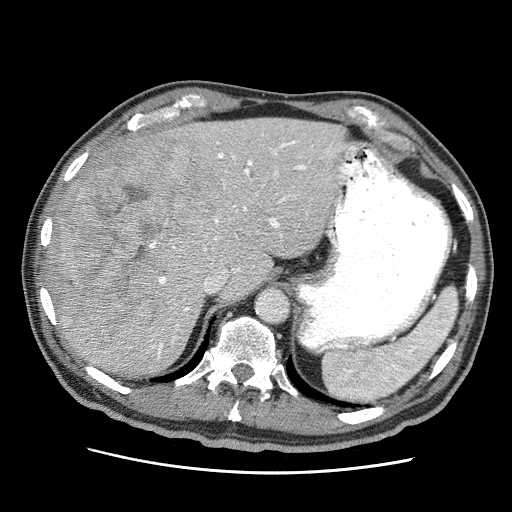
Contrast-enhanced abdominal CT (liver protocol), one axial slice. Position 43 of 75 along the scan axis. Reconstruction kernel STANDARD. 120 kVp. Soft-tissue window (W 400 / L 40 HU). 2.5 mm slice thickness. 512 × 512 image matrix, field of view 360 × 360 mm. From the clinical record (not read from this slice): diagnosis: hepatocellular carcinoma (patient treated with transarterial chemoembolisation; whether this scan precedes or follows treatment is not stated here); TNM stage (as recorded): Stage-IIIA; Child-Pugh class: A; tumour size: 13.9 cm.
Outlined on this slice (semi-automatically segmented with operator editing):
- liver parenchyma outside the tumour (the mass and vessels are separate outlines, so this box may not span the whole liver): bounding box [x1, y1, x2, y2] px = [48, 118, 346, 376]
- mass: [50, 136, 221, 354]
- liver vessels: [147, 134, 333, 359]